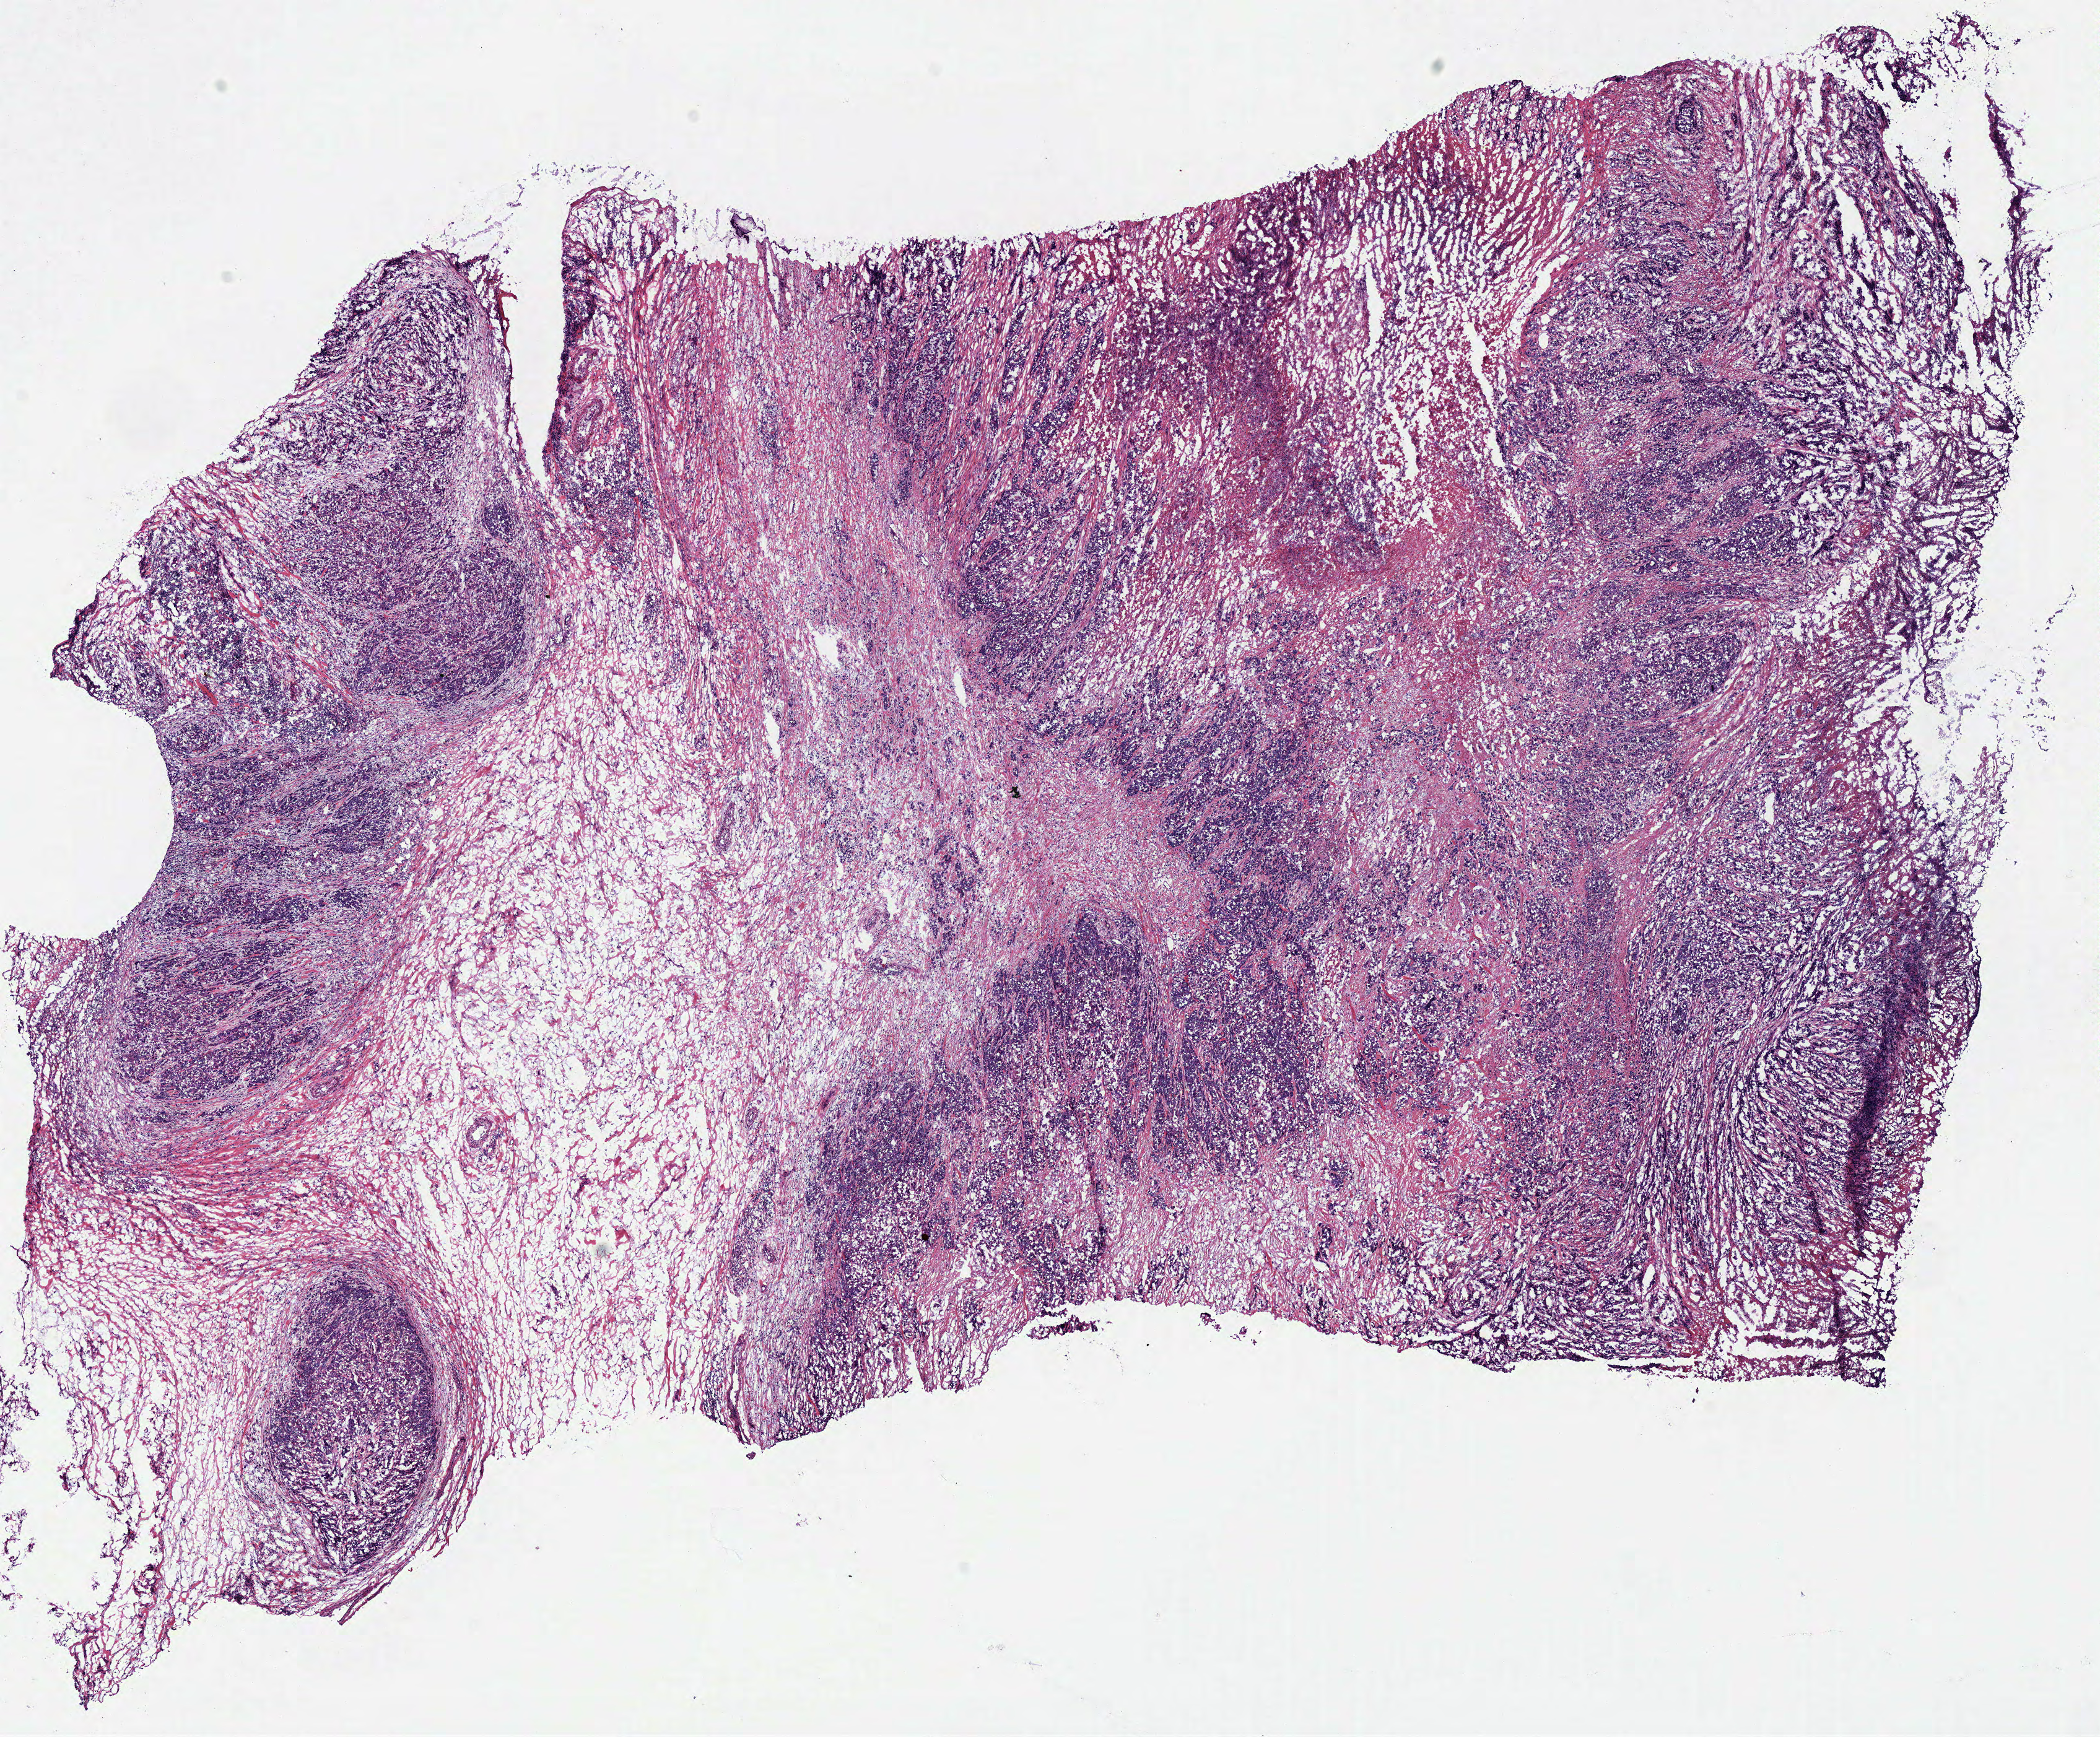
H&E whole-slide image, a low-resolution overview of the entire scanned area, about 13.4 x 11.1 mm. Frozen section from the bottom of the tissue portion. Primary tumour sample from the stomach. Patient: male, age at initial diagnosis 45 years. Histologic grade: G3 (poorly differentiated). Pathologist review of this section (percent, as recorded): tumour cells 72%, tumour nuclei 80%, normal cells 0%, stromal cells 20%, necrosis 8%.
• histologic diagnosis: Adenocarcinoma, intestinal type (gastric antrum)
• TNM: T2 N1 M0
• AJCC pathologic stage: II (6th edition)